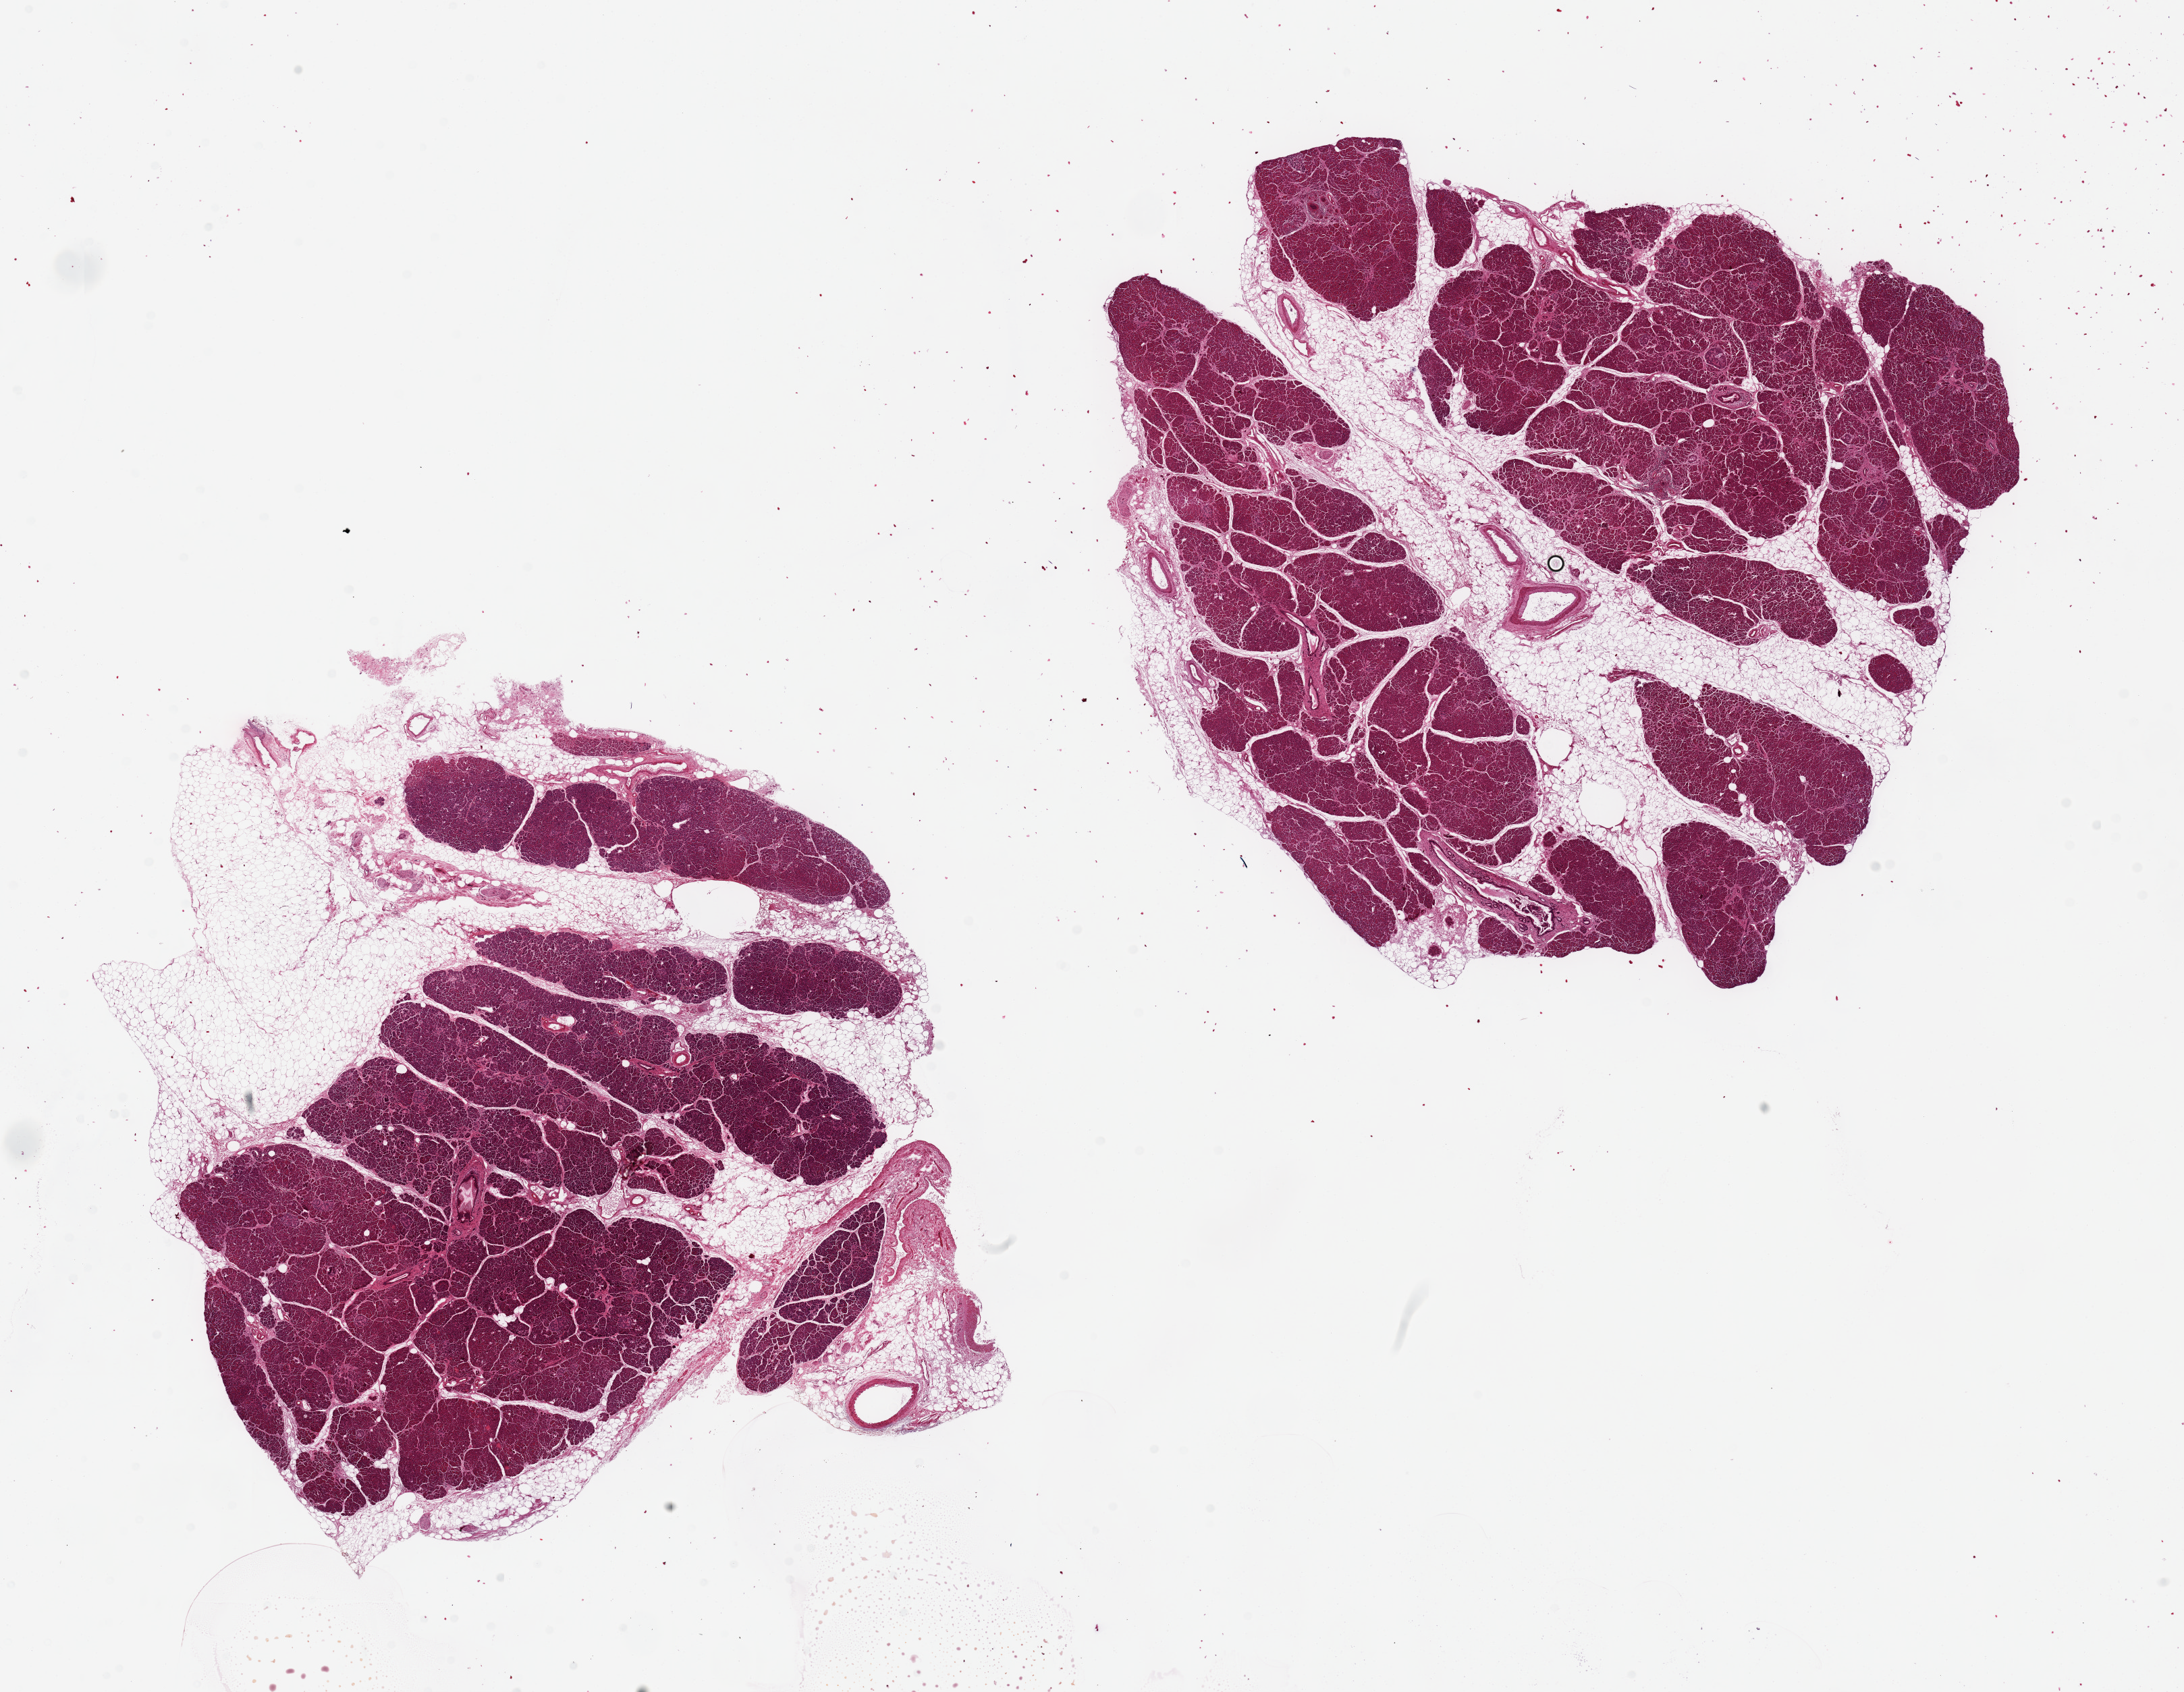
Haematoxylin and eosin whole-slide image, brightfield — a low-resolution overview of the entire scanned area, about 25.6 x 19.8 mm (from a 20x scan), PAXgene-fixed paraffin-embedded (PFPE) section, section of pancreas (target tissue), donor tissue sample. Donor: male.
Pathologist's review note for this sample: 2 pieces, 12x10 & 11x11mm; 20% intraglandular adipose.